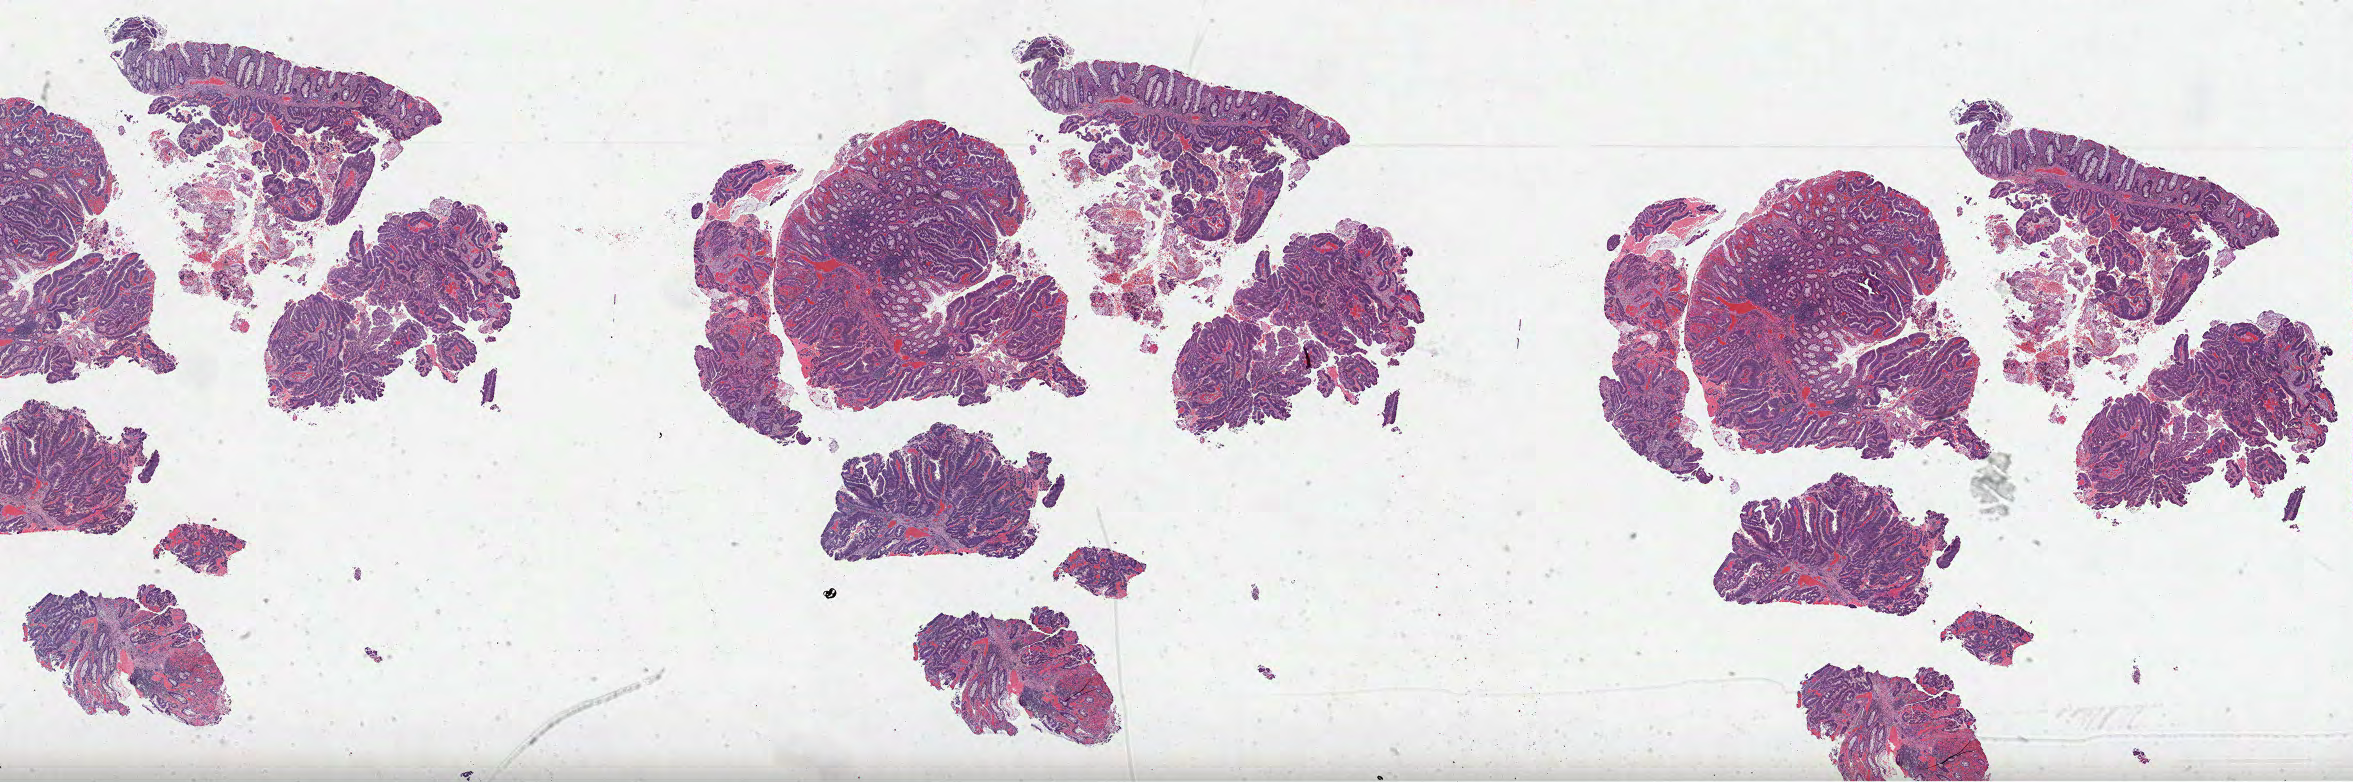
Digitized H&E tissue section (whole slide) — whole scanned area (about 38.0 x 12.6 mm, from a 40x scan) shown as a low-resolution overview, formalin-fixed paraffin-embedded (FFPE) diagnostic section, sample: primary tumour, rectum. Male patient; age at initial diagnosis 43 years.
• AJCC pathologic stage: IV (7th edition)
• diagnosis: Adenocarcinoma, NOS (rectosigmoid junction)